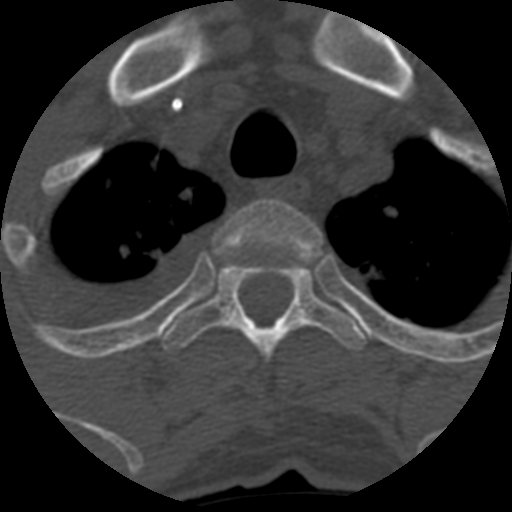
CT including the spine, one axial slice. Position 493 of 708 along the scan axis. One of 3 acquisitions stored at this slice position. Bone window (W 1800 / L 400 HU). 1.25 mm slice thickness. 512 × 512 image matrix, field of view 160 × 160 mm. Patient age 55 years. Case-level facts recorded for this patient, not image findings: primary cancer: colon.
Outlined on this slice (semi-automatically segmented with operator editing):
- T2 vertebra: bounding box [x1, y1, x2, y2] px = [220, 200, 322, 262]
- T3 vertebra: [161, 256, 366, 363]